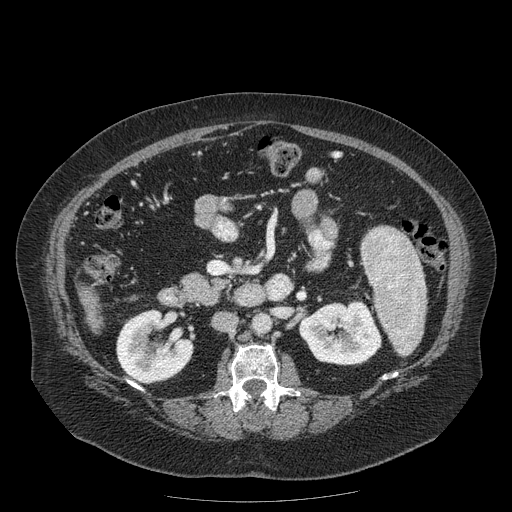
Contrast-enhanced abdominal CT (liver protocol), one axial slice. Slice 51 of 204 in the series (ordered by position). Soft-tissue window (W 400 / L 40 HU). 2.5 mm slice thickness. 512 × 512 image matrix. From the clinical record (not read from this slice): diagnosis: hepatocellular carcinoma (patient treated with transarterial chemoembolisation; whether this scan precedes or follows treatment is not stated here); TNM stage (as recorded): Stage-IIIB; Child-Pugh class: A; tumour differentiation: well differentiated; tumour nodularity: uninodular.
Outlined on this slice (semi-automatic segmentation, software-assisted and operator-edited):
- liver parenchyma outside the tumour (the mass and vessels are separate outlines, so this box may not span the whole liver): bounding box (x1, y1, x2, y2) in pixels: (80, 288, 102, 332)